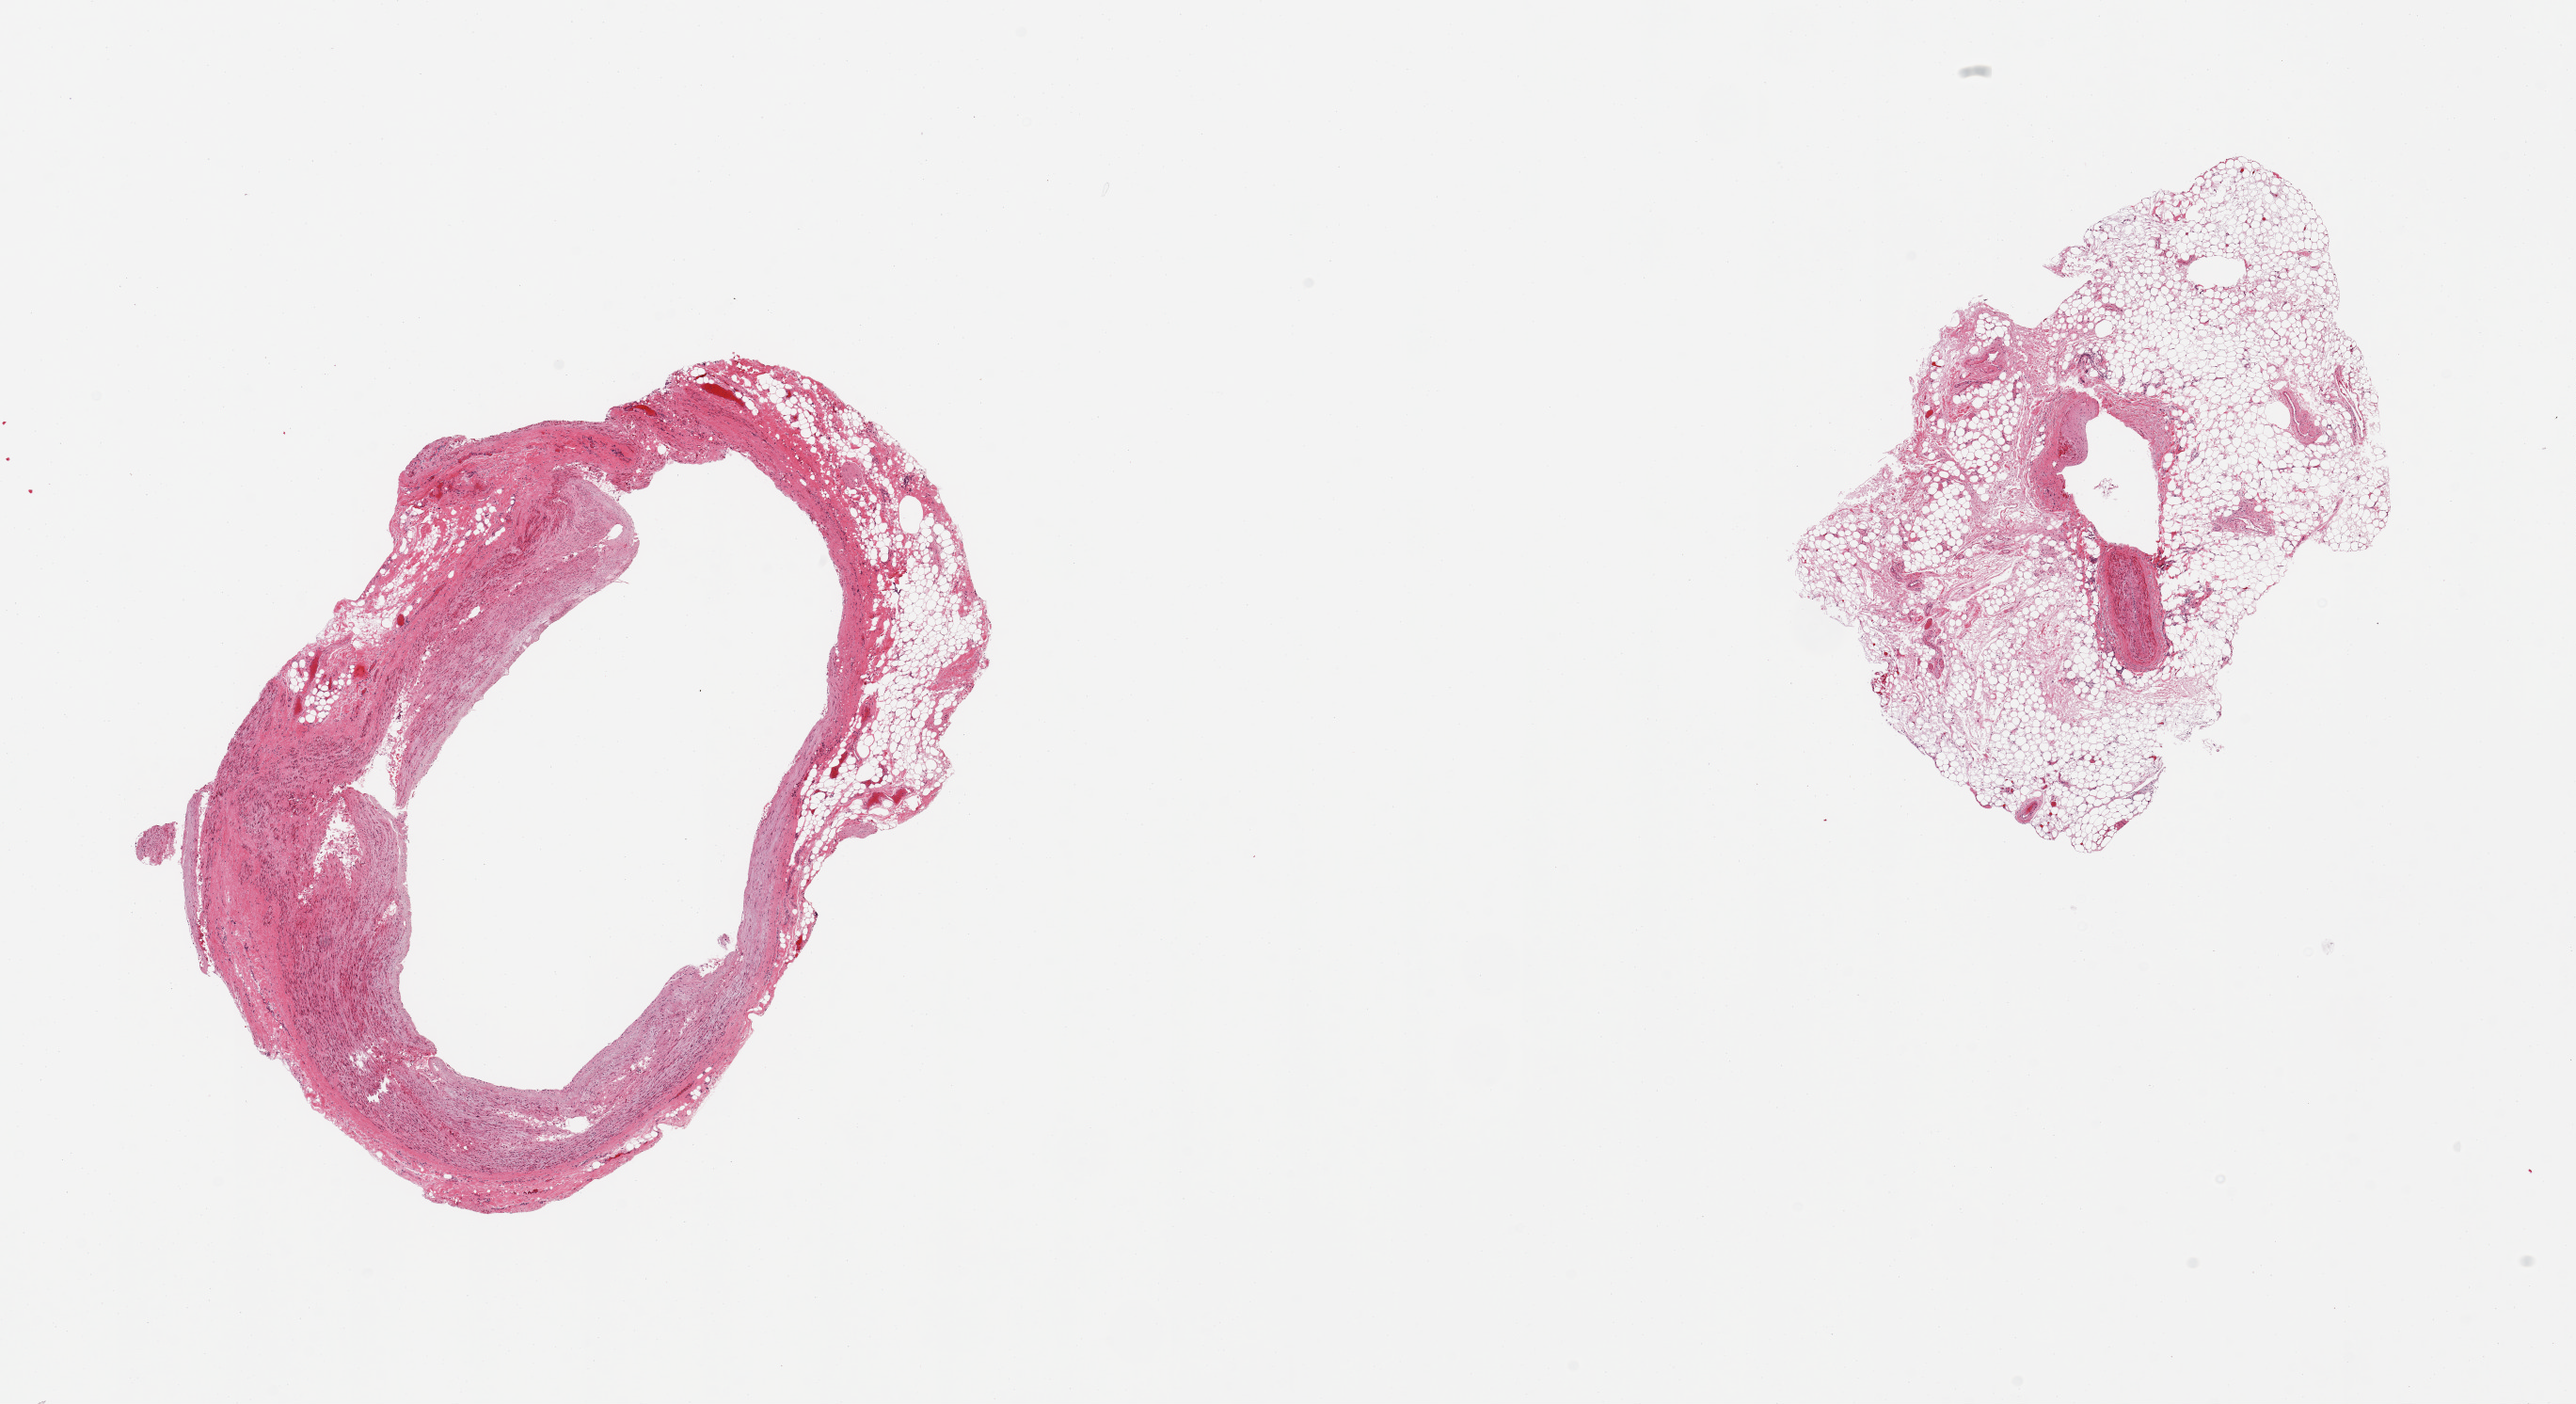
Digitized haematoxylin and eosin-stained section, shown as a low-resolution overview of the whole scanned area (about 21.7 x 11.8 mm). PAXgene-fixed, paraffin-embedded tissue. Section of coronary artery (target tissue). Donor tissue sample. Male donor.
* pathologist's review note for this sample: 2 pieces; 1 sclerotic with 20% external fat; other 80% external fat